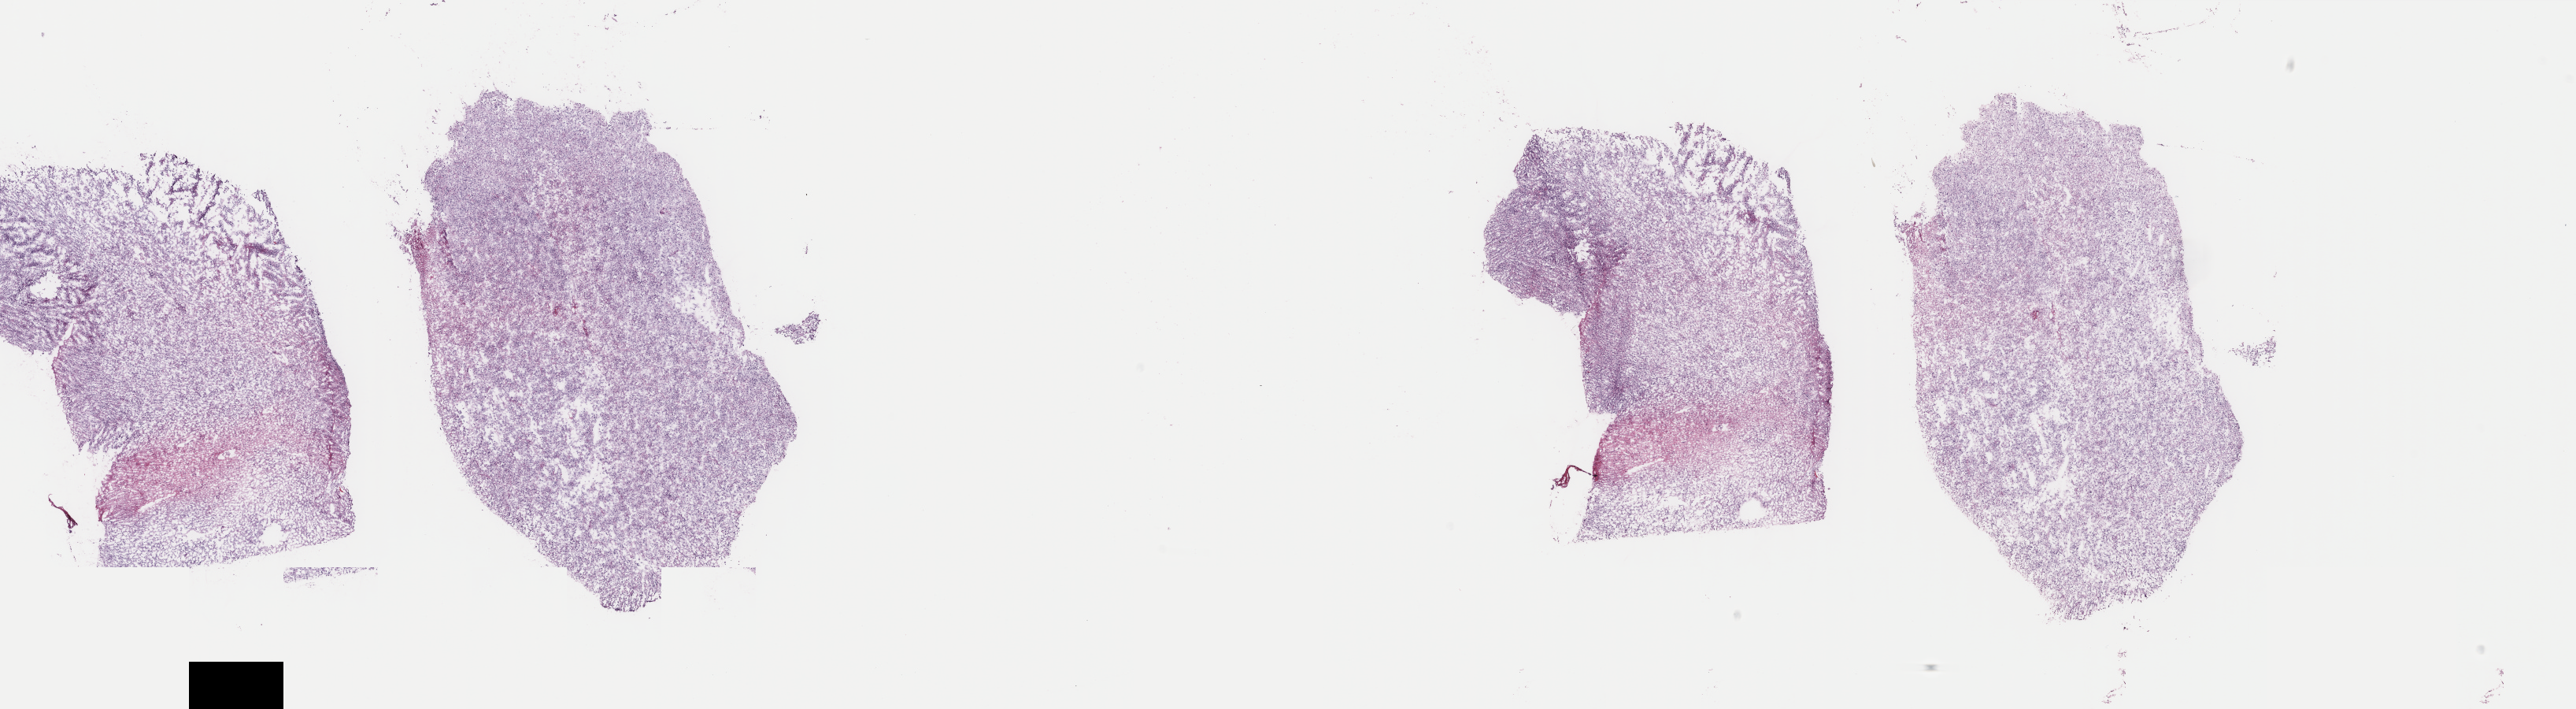
Whole-slide histology image, H&E-stained, a low-resolution overview of the entire scanned area, about 26.0 x 7.1 mm (acquisition: 40x scan); frozen section from the top of the tissue portion; primary tumour sample from the brain. Patient: male, age at initial diagnosis 51 years.
Histologic diagnosis: Oligodendroglioma, NOS (cerebrum).